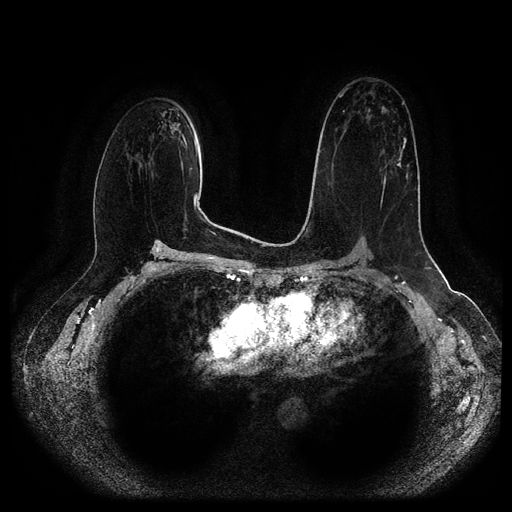
Breast MRI (dynamic contrast-enhanced, multi-phase), one axial slice. Dynamic contrast-enhanced series, time point 2 of 5 at this slice position (early post-contrast). 1.5 T. TE 2.6 ms, TR 5.2 ms. 2 mm slice thickness. 512 × 512 image matrix, field of view 380 × 380 mm. Patient: female, 57 years.
Outlined on this slice (semi-automatically segmented with operator editing):
- breast lesion (labelled 'tumour' in the annotation; benign lesions carry a separate 'benign' label): box from (x=395, y=137) to (x=407, y=168) px